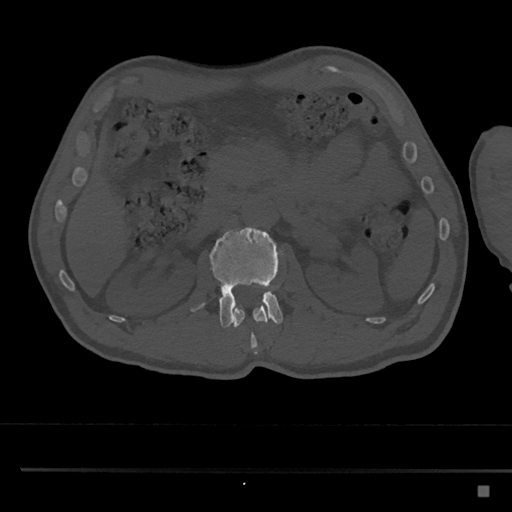
CT including the spine, one axial slice; position 786 of 797 along the scan axis; reconstruction kernel Br40s/3; 120 kVp; bone window (W 1800 / L 400 HU); 0.5 mm slice thickness; 512 × 512 image matrix, field of view 391 × 391 mm. Male patient, age 59 years. From the clinical record (not read from this slice): primary cancer: prostate.
Annotated regions visible in this slice (semi-automatic segmentation, software-assisted and operator-edited):
- L1 vertebra: bounding box [x1, y1, x2, y2] px = [233, 302, 268, 354]
- L2 vertebra: [190, 227, 285, 328]